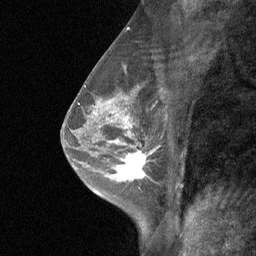
Breast MRI (dynamic contrast-enhanced), one sagittal slice; slice 38 of 64 in the series (ordered by position); dynamic contrast-enhanced study with each time point stored as its own series, time point 2 of 3 at this slice position (early post-contrast, ordered by acquisition time); 1.5 T; TE 4.8 ms, TR 27 ms; 256 × 256 image matrix, field of view 180 × 180 mm. Female patient, age 47 years. From the clinical record (not read from this slice): setting: breast cancer imaged before/during neoadjuvant chemotherapy; receptor status: HR-positive, HER2-negative.
Structures marked on this image (semi-automatic segmentation, software-assisted and operator-edited):
- analysis volume of interest (the breast-tissue region the enhancement analysis was run in; not a lesion): box from (x=104, y=138) to (x=161, y=198) px
- tumour enhancement mask (voxels above the 90 % enhancement threshold inside the analysis volume of interest): (x=110, y=141)–(x=153, y=181)